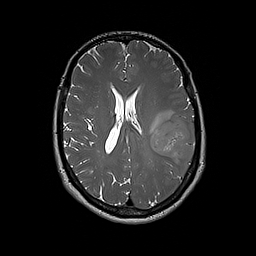
Brain MRI from a brain-tumour surgery series, one axial slice; slice 87 of 192 in the series (ordered by position); 1 mm slice thickness; 256 × 256 image matrix, field of view 250 × 250 mm. From the clinical record (not read from this slice): histopathology: Glioblastoma; WHO grade: 4; IDH mutation: no; tumour location: Left Frontal.
Outlined on this slice (expert manual segmentation):
- tumour: bounding box (x1, y1, x2, y2) in pixels: (151, 116, 195, 165)